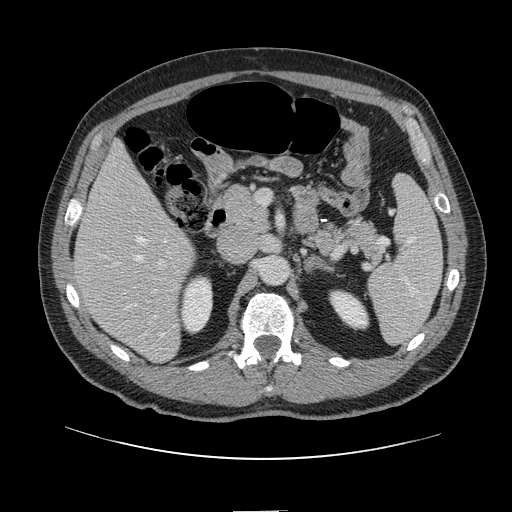
Contrast-enhanced abdominal CT, one axial slice. Slice 62 of 161 in the series (ordered by position). 120 kVp. Intravenous contrast given. Soft-tissue window (W 400 / L 40 HU). 2.5 mm slice thickness. 512 × 512 image matrix, field of view 412 × 412 mm. Male patient, age 66 years. From the clinical record (not read from this slice): diagnosis: colorectal cancer liver metastases, imaged before liver resection.
Structures marked on this image (manually delineated by an expert):
- hepatic veins: bounding box <126,236,164,336> (left, top, right, bottom; pixels)
- liver: <75,144,195,362>
- planned liver remnant (the part of the liver to remain after resection): <75,144,174,285>
- portal vein (with intrahepatic branches): <151,259,167,293>